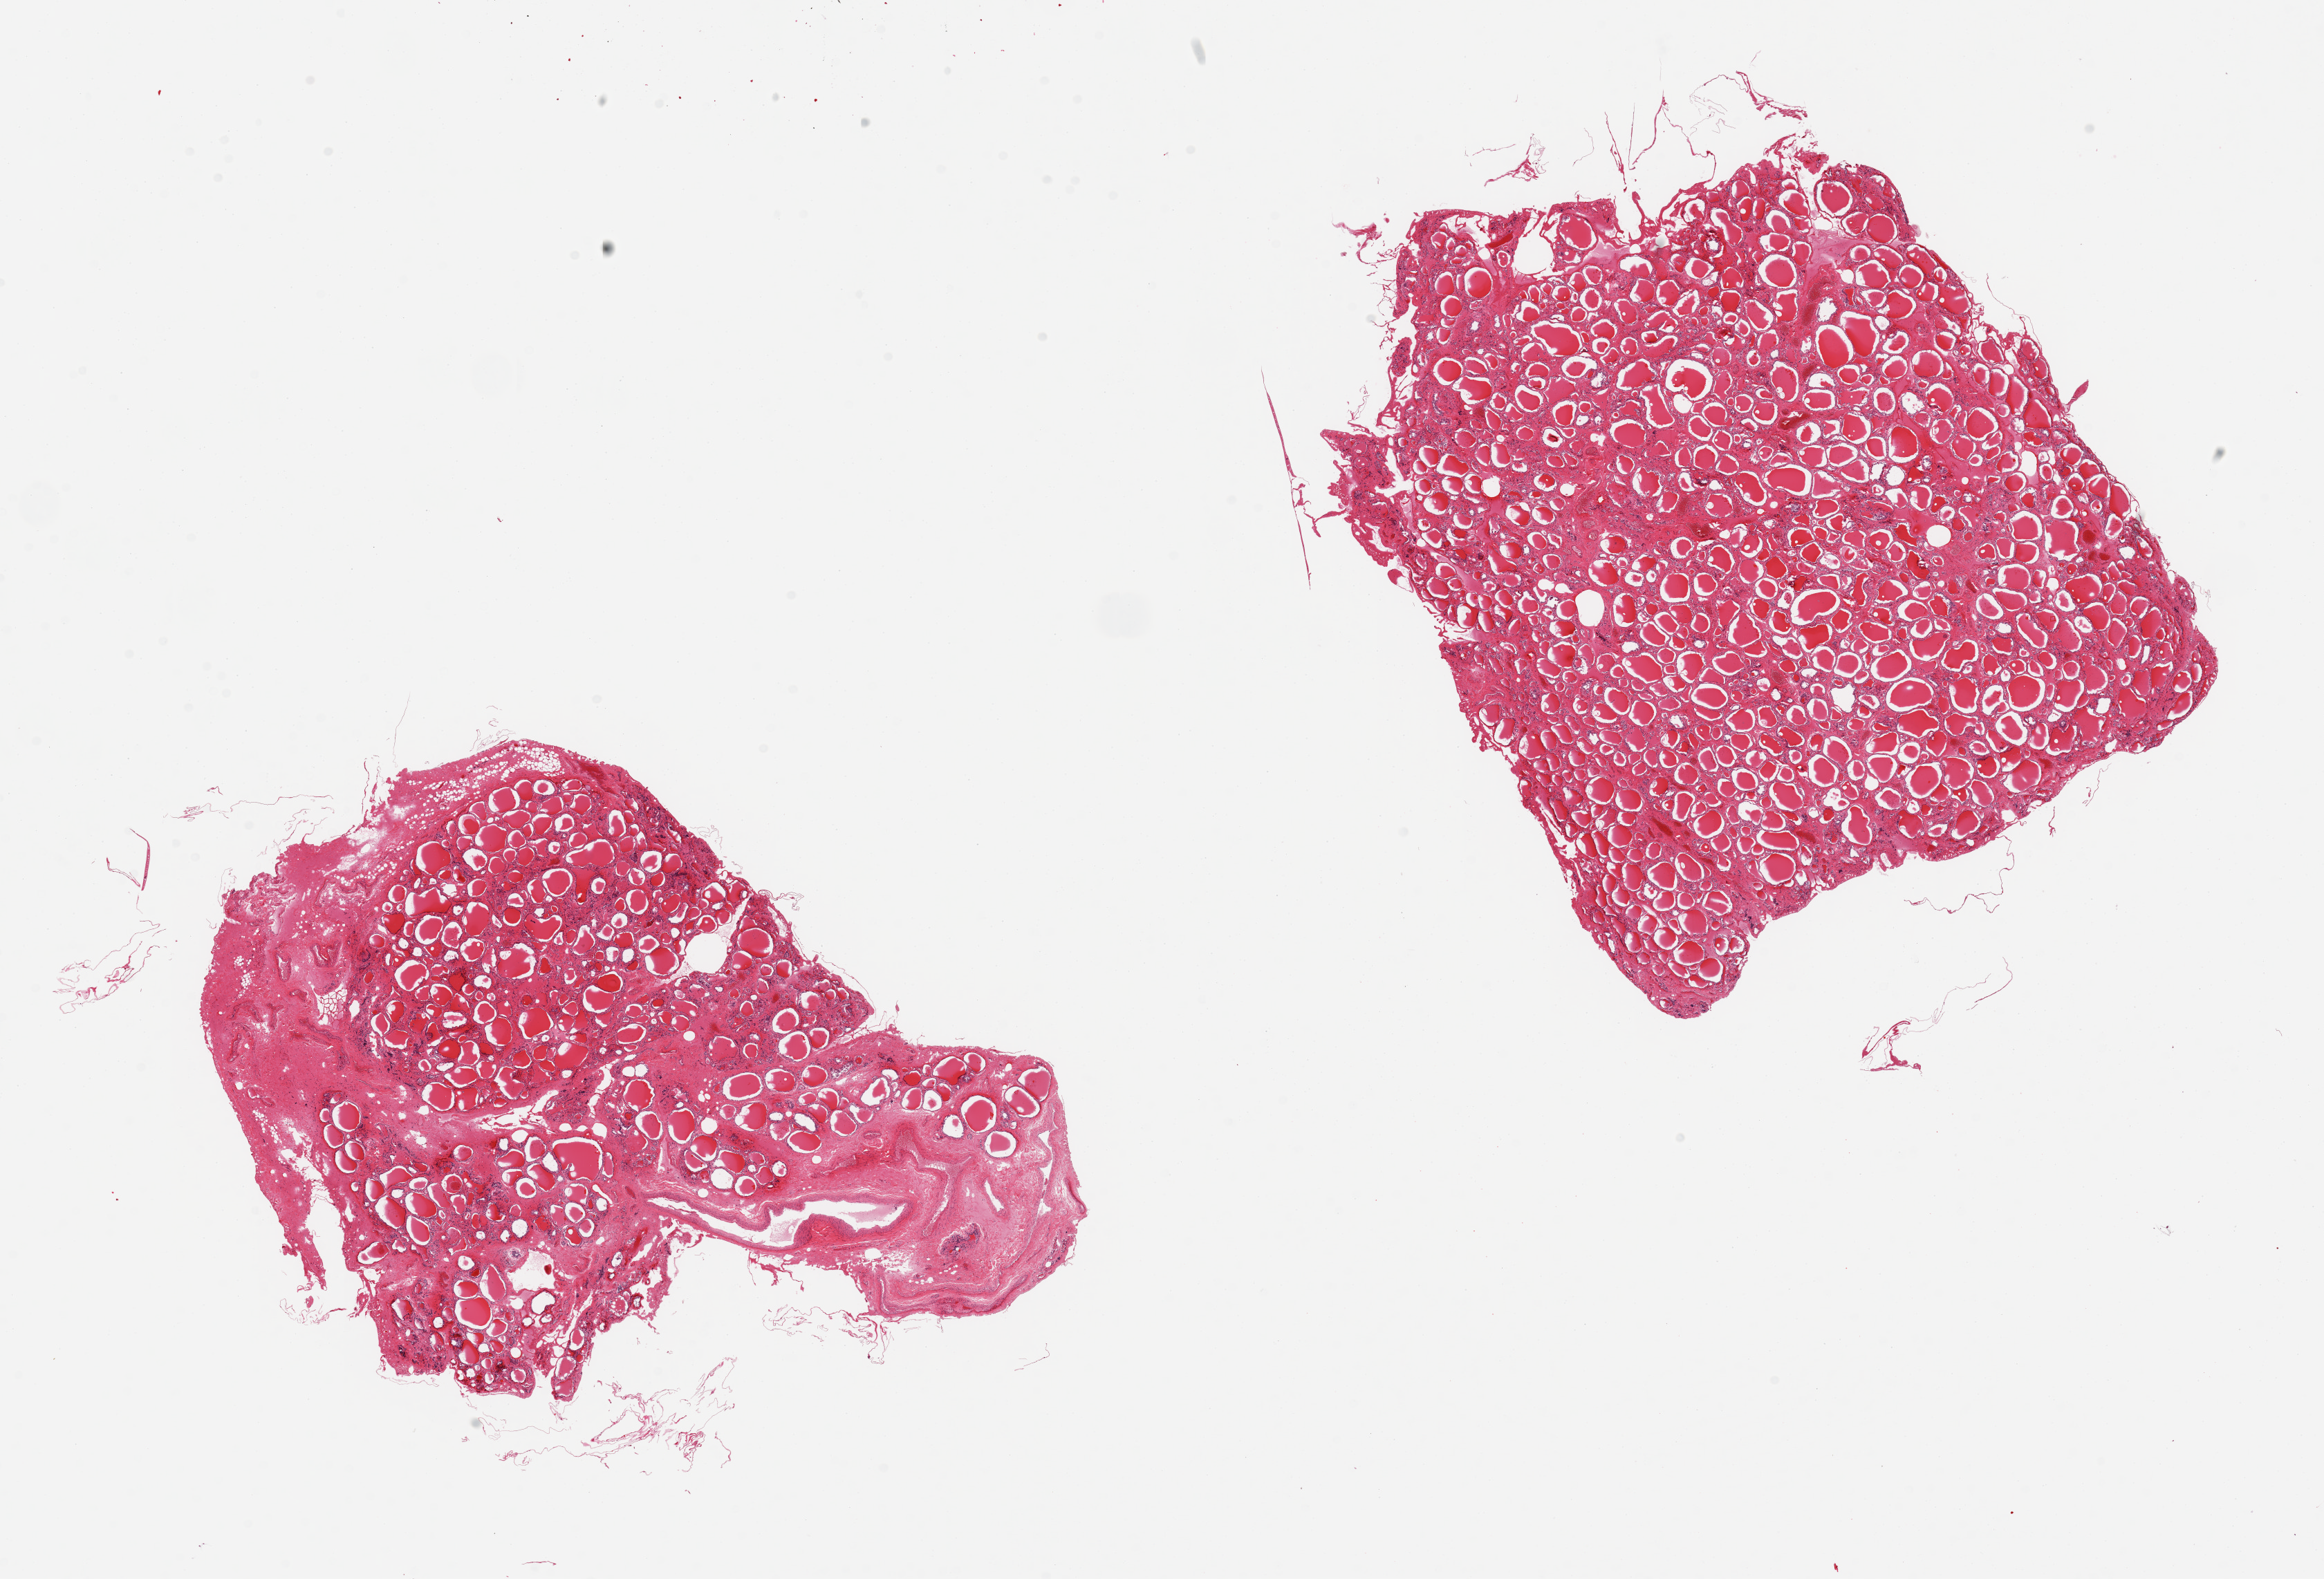
Digitized haematoxylin and eosin-stained section, brightfield — a low-resolution overview of the entire scanned area, about 26.6 x 18.1 mm (from a 20x scan), PAXgene-fixed, paraffin-embedded tissue, section of thyroid (target tissue), donor tissue sample. Donor: male.
Reviewer comment on this tissue sample: 2 pieces.